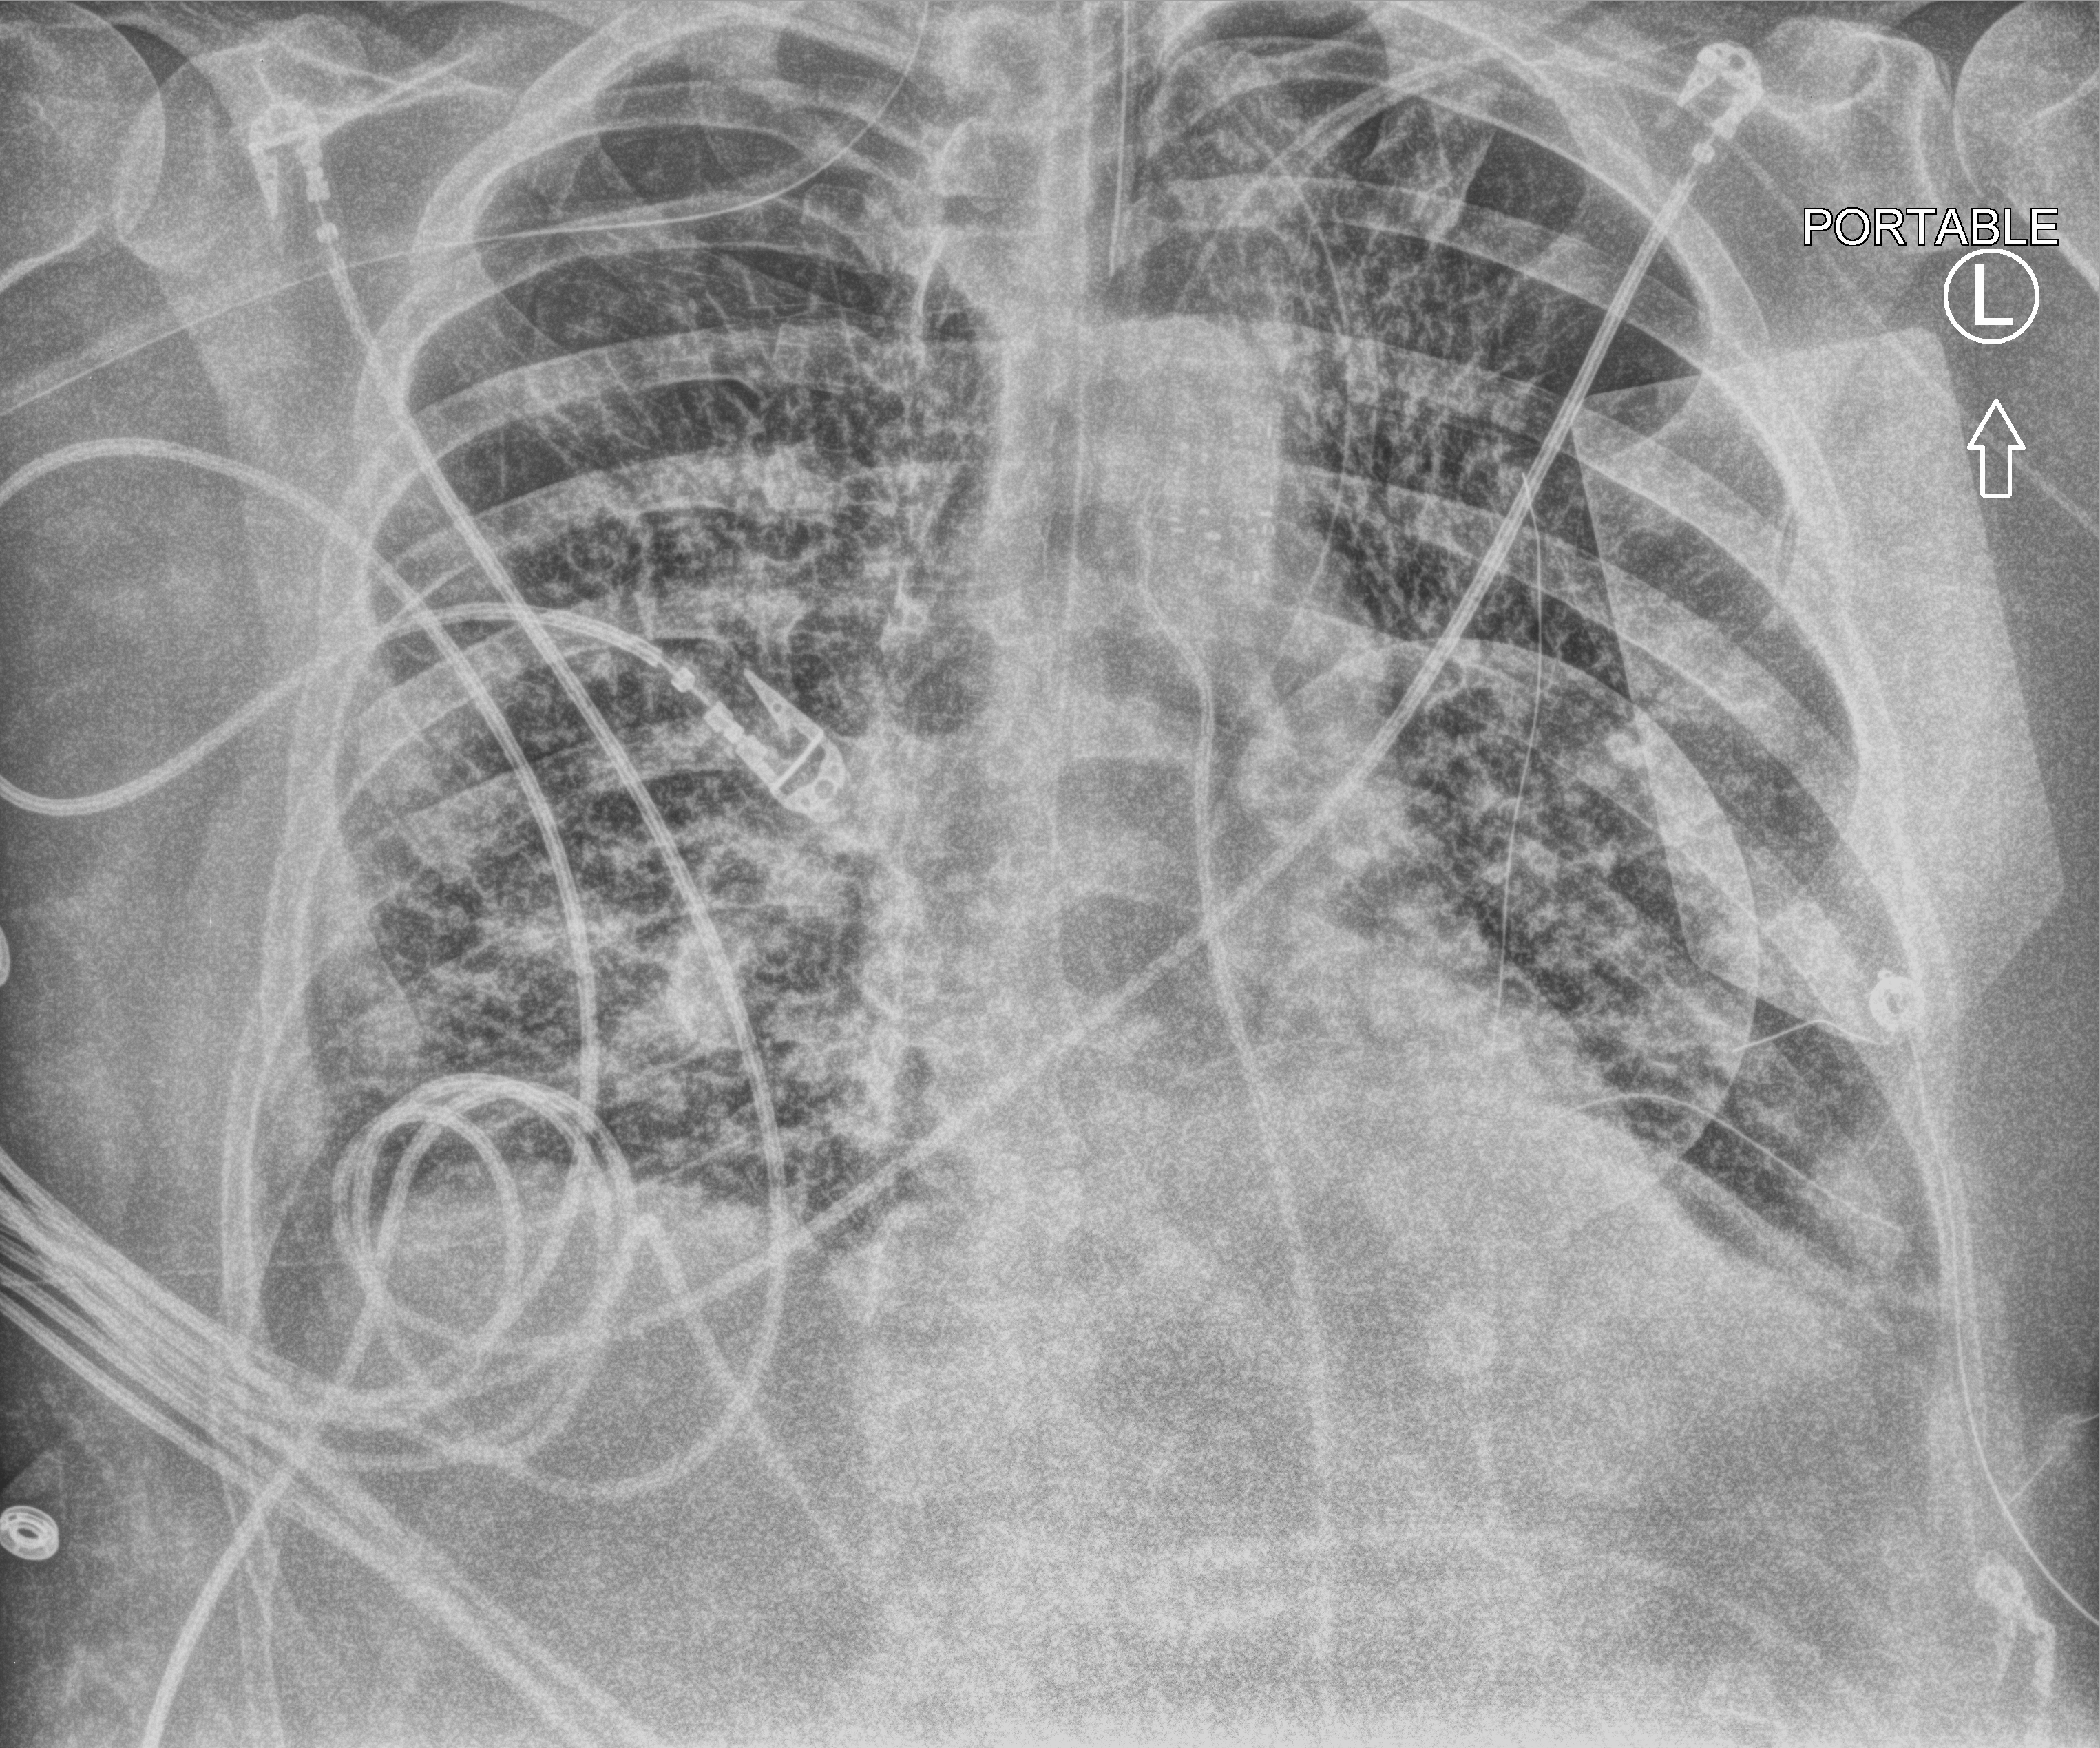
Portable chest radiograph; anteroposterior (AP) projection. Adult patient hospitalised with COVID-19, age 18–59 years.
From the hospital-stay record, not from the radiograph (when in the stay this image was taken is not recorded): length of hospital stay: 9 days.